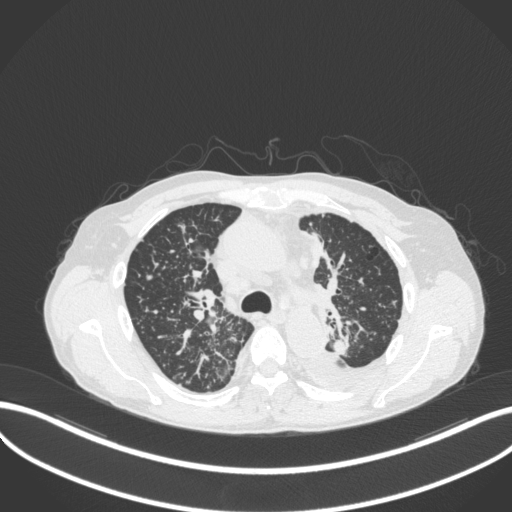
Chest CT, one axial slice; position 248 of 319 along the scan axis; reconstruction kernel B31f; 120 kVp; lung window (W 1500 / L -600 HU); 1 mm slice thickness; 512 × 512 image matrix. Patient: male, 58 years. From the clinical record (not read from this slice): clinical TNM (as recorded): T1c N3 M1.
Structures marked on this image (rectangle marked by the reading radiologist):
- lung tumour (recorded histology: adenocarcinoma): bounding box [x1, y1, x2, y2] px = [333, 335, 355, 358]